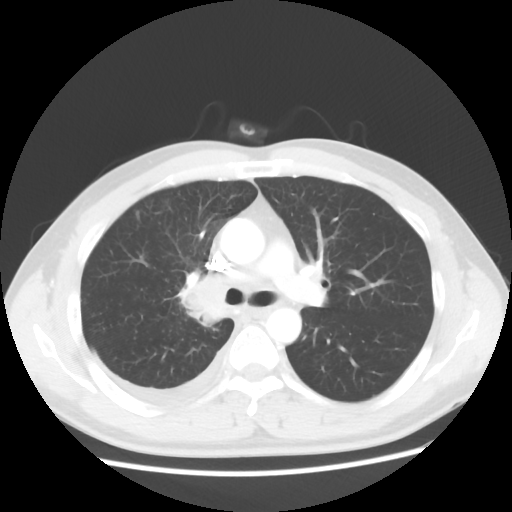
Chest CT, one axial slice; lung window (W 1500 / L -600 HU); 5 mm slice thickness; 512 × 512 image matrix. Male patient, age 46 years. Case-level facts recorded for this patient, not image findings: clinical TNM (as recorded): T2 N3 M1.
Annotated regions visible in this slice (bounding box drawn by a radiologist):
- lung tumour (recorded histology: adenocarcinoma): bounding box <185,274,228,332> (left, top, right, bottom; pixels)